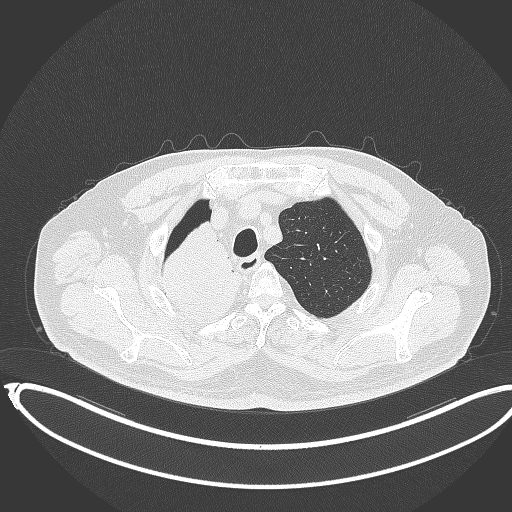
Chest CT, one axial slice. Reconstruction kernel B70f. 120 kVp. Lung window (W 1500 / L -600 HU). 1 mm slice thickness. 512 × 512 image matrix, field of view 436 × 436 mm. Male patient, age 68 years. Case-level facts recorded for this patient, not image findings: clinical TNM (as recorded): T2a N0 M0.
Outlined on this slice (bounding box drawn by a radiologist):
- lung tumour (recorded histology: adenocarcinoma): bounding box [x1, y1, x2, y2] px = [158, 222, 244, 325]